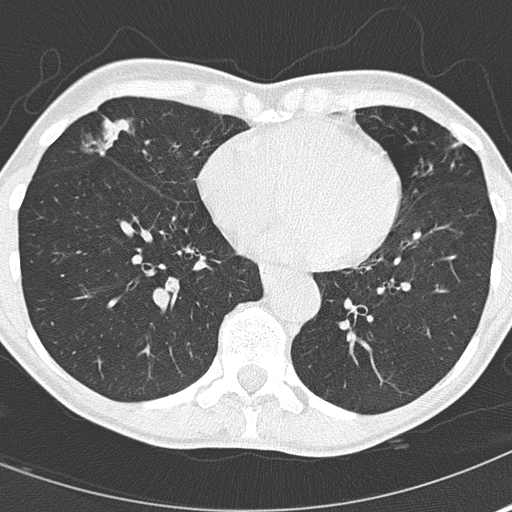
Chest CT (low-dose screening protocol), one axial image. Second screening round (one year after baseline). Lung window (W 1500 / L -600 HU). 2 mm slice thickness. Lung (sharp) reconstruction kernel (B50f). Slice 108 of 167 in the series. Female, age 67 years at enrolment. Current smoker at enrolment.
Expert-annotated lung lesion, bounding box (x1, y1, x2, y2) in pixels: (84, 107, 192, 197). The screening reader recorded 2 non-calcified nodules or masses ≥4 mm on this exam; which of them this box marks is not recorded. Official screen result: positive, other. Participant outcome: lung cancer diagnosed 475 days after this screen — bronchiolo-alveolar adenocarcinoma, NOS, right middle lobe, well differentiated (G1), stage IA (AJCC 6th edition), 25 mm at pathology.